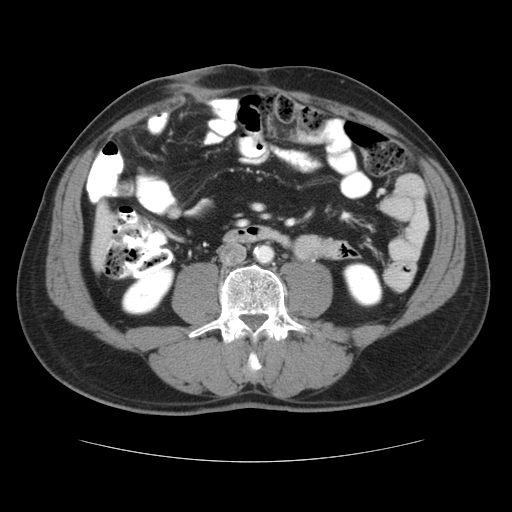
Contrast-enhanced abdominal CT, one axial slice. Position 5 of 37 along the scan axis. Intravenous contrast given. Soft-tissue window (W 400 / L 40 HU). 5 mm slice thickness. 512 × 512 image matrix. Male patient, age 66 years. Case-level facts recorded for this patient, not image findings: diagnosis: colorectal cancer liver metastases, imaged before liver resection; multiple liver metastases: yes; largest metastasis: 1.6 cm; disease in both lobes: yes.
Structures marked on this image (expert manual segmentation):
- liver: bounding box <92,202,114,269> (left, top, right, bottom; pixels)
- planned liver remnant (the part of the liver to remain after resection): <93,203,114,269>